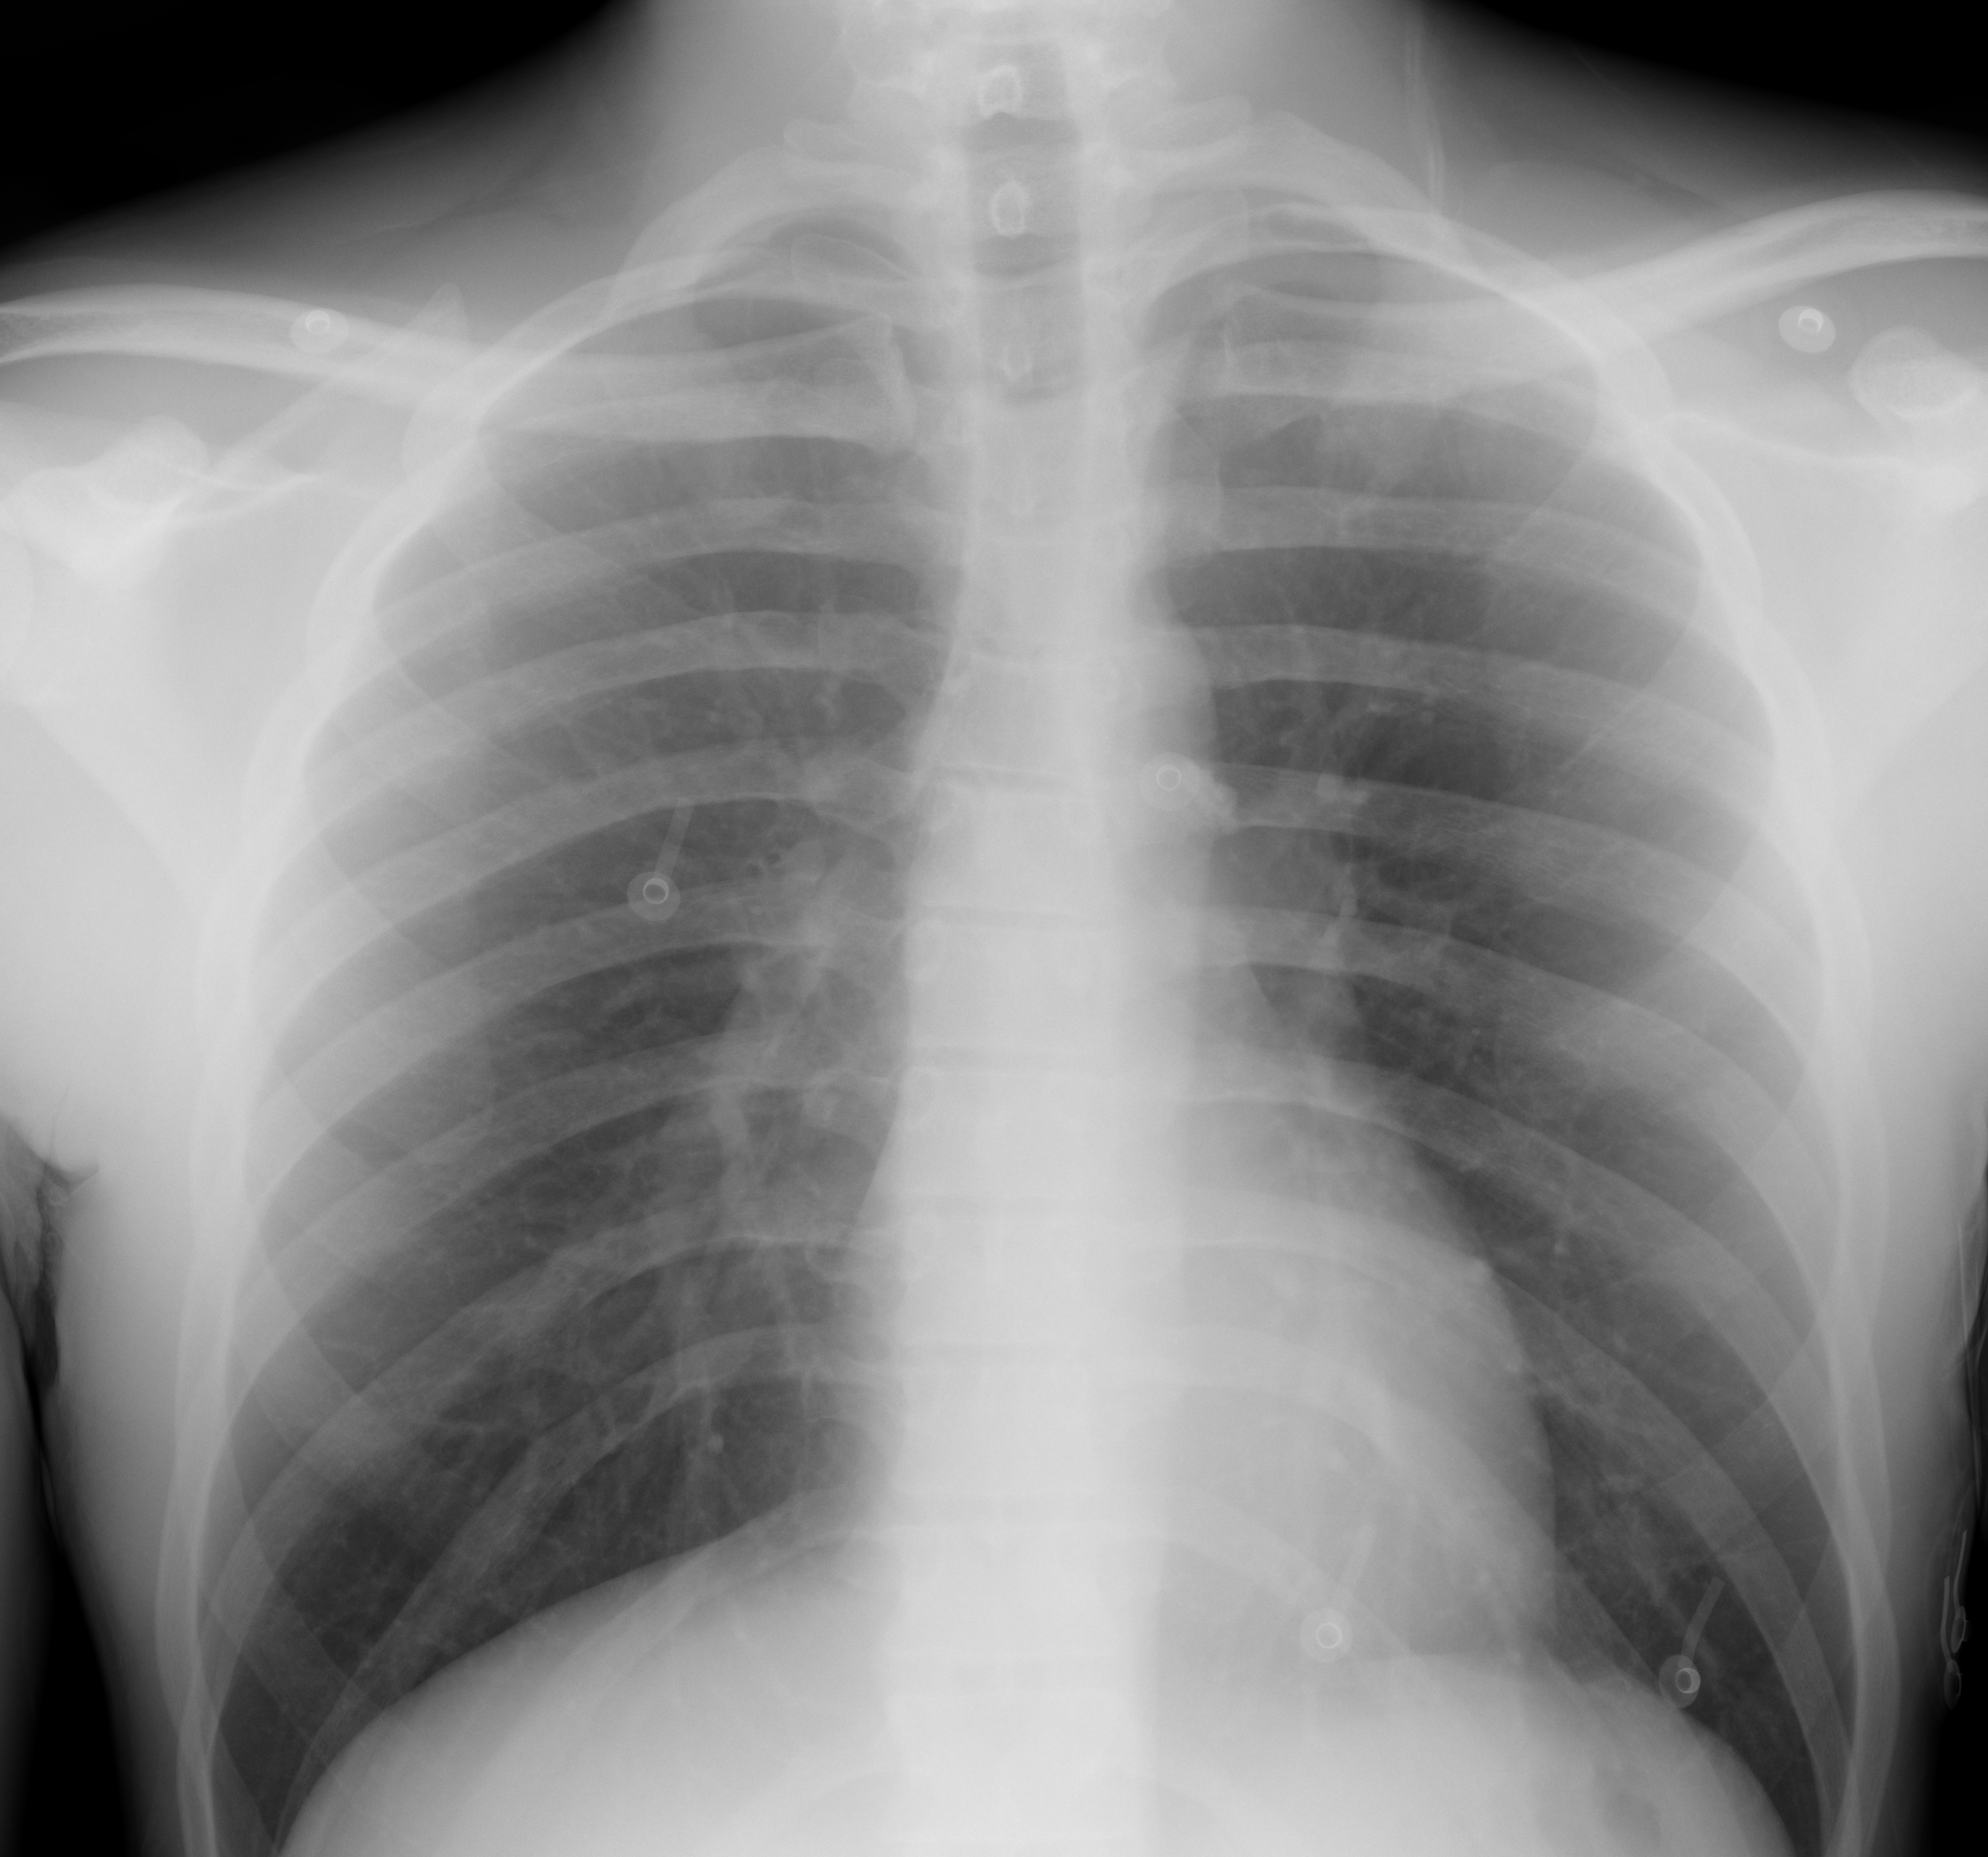
Chest X-ray (portable), AP projection. Male patient, age 19 years; imaged 1 day after the COVID-19 diagnosis.
Radiologist's key findings for this exam: The lungs are clear.